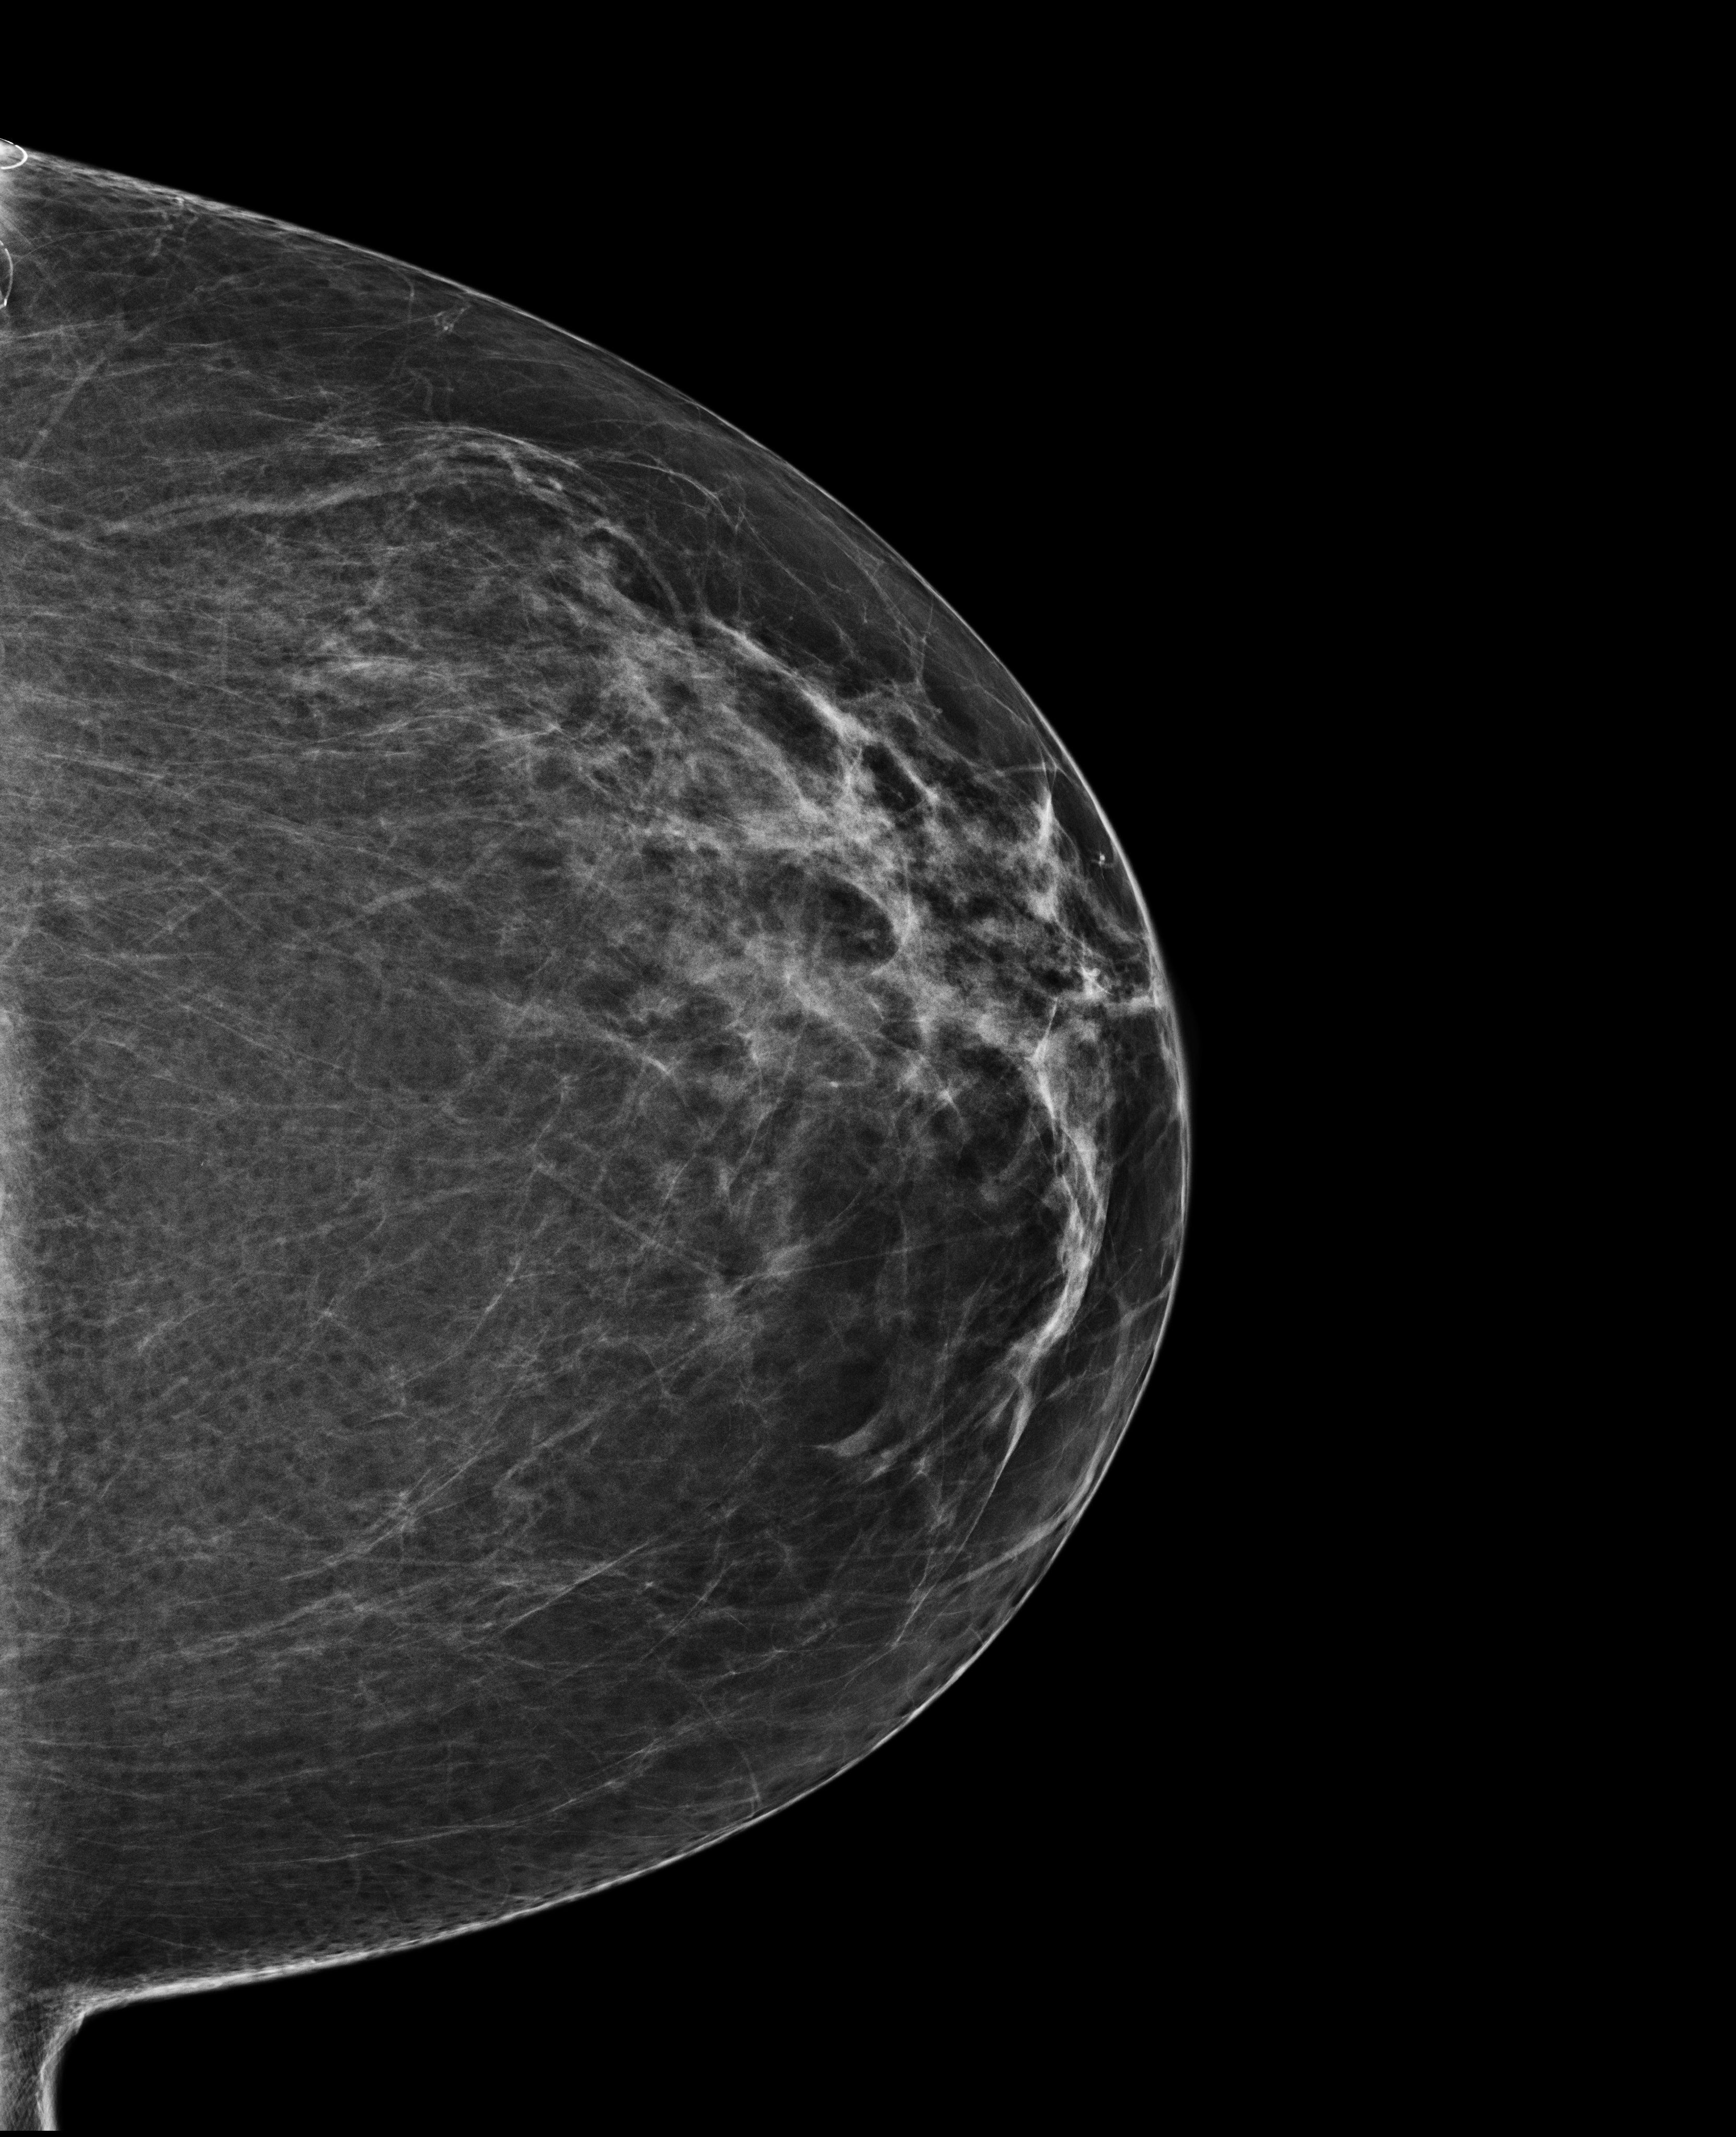
Screening examination, system: Selenia Dimensions. Female patient, age 67 years.
Image type: full-field digital mammogram. Breast: left. Projection: craniocaudal (CC) view.